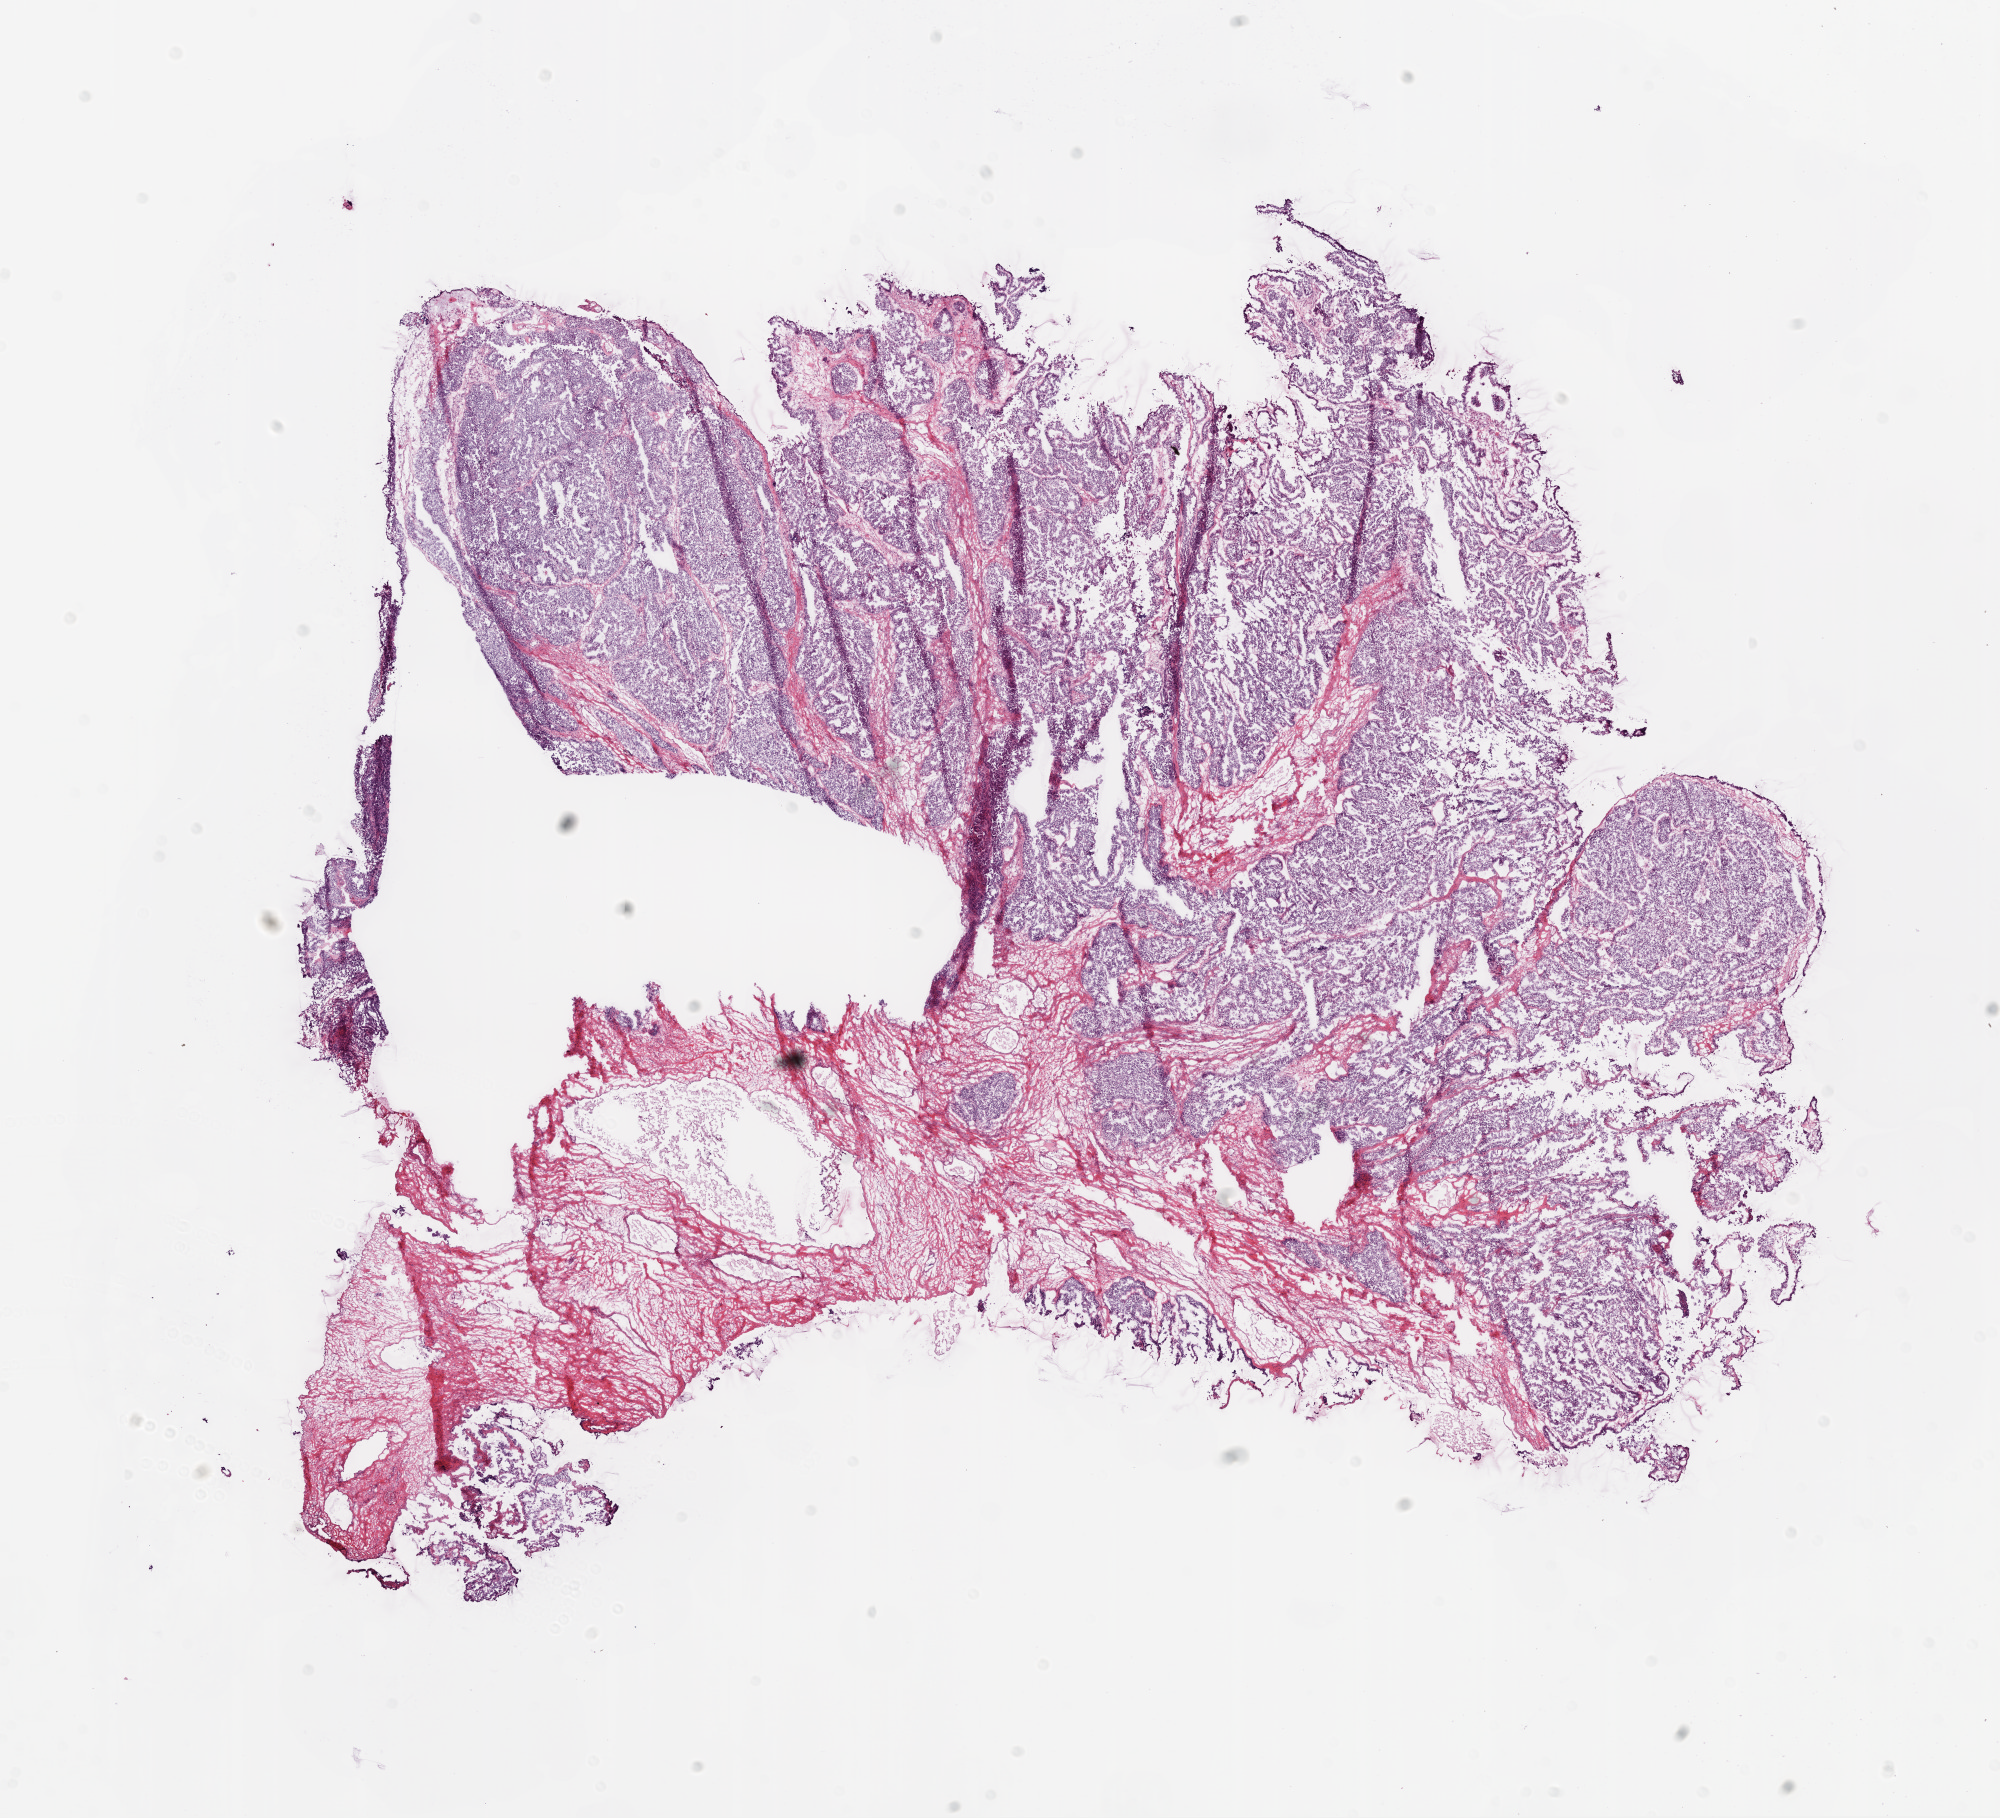
Hematoxylin and eosin (H&E) stained whole-slide image — whole scanned area (about 16.0 x 14.6 mm, from a 20x scan) shown as a low-resolution overview, frozen section from the bottom of the tissue portion, sample: primary tumour, ovary. Patient: female, age at initial diagnosis 51 years. Histologic grade: G2 (moderately differentiated). Pathologist review of this section (percent, as recorded): tumour cells 75%, tumour nuclei 90%, normal cells 0%, stromal cells 25%, necrosis 0%. Inflammatory infiltration, as recorded: lymphocyte infiltration 5%.
FIGO stage: IIIC. Diagnosis: Serous cystadenocarcinoma, NOS. Laterality: bilateral.